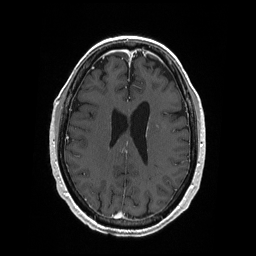
Brain MRI from a brain-tumour surgery series, one axial slice; slice 80 of 208 in the series (ordered by position); T1-weighted post-contrast; 1 mm slice thickness; 256 × 256 image matrix, field of view 256 × 256 mm. Case-level facts recorded for this patient, not image findings: histopathology: Primary diffuse large B-cell lymphoma.
Structures marked on this image (manually delineated by an expert):
- tumour: bounding box <156,124,159,129> (left, top, right, bottom; pixels)